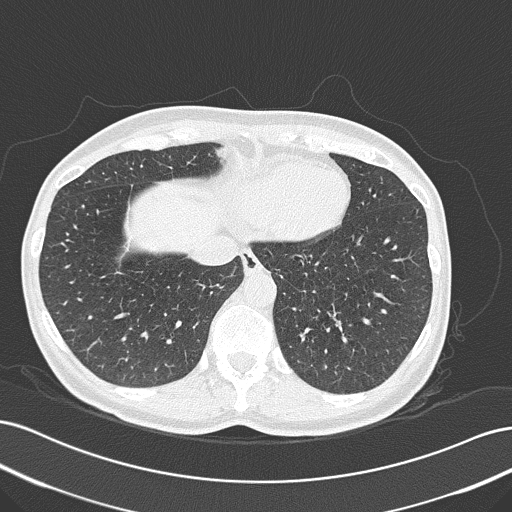
Low-dose screening chest CT, axial slice, first (baseline) screen, lung window (W 1500 / L -600 HU), 2 mm slice thickness, slice 125 of 185 in the series, 512 × 512 image matrix, field of view 360 × 360 mm. Female, age 55 years at enrolment. Current smoker at enrolment.
Lesion marked by an expert reader, box from (x=323, y=307) to (x=358, y=341) px. Reader record for this screening exam (exam-level; its link to the box is not recorded): non-calcified nodule or mass ≥4 mm, right upper lobe, 14 × 7 mm, spiculated (stellate) margins, ground glass attenuation. Note: the box lies in the patient's left hemithorax on this image, whereas the reader's record names the right lung; they may be different findings. Lung cancer was diagnosed 1065 days after this screen (after the third annual screen): adenocarcinoma, NOS, left lower lobe, well differentiated (G1), stage IA (AJCC 6th edition), 11 mm at pathology.